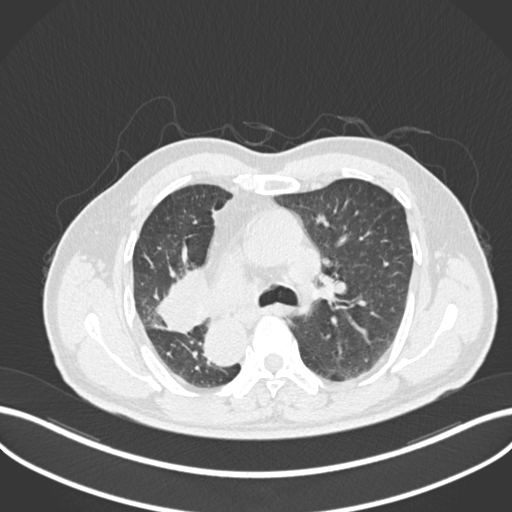
Chest CT, one axial slice; position 152 of 206 along the scan axis; 120 kVp; lung window (W 1500 / L -600 HU); 1 mm slice thickness; 512 × 512 image matrix. Patient: male, 67 years. From the clinical record (not read from this slice): clinical TNM (as recorded): T2a N0 M0.
Outlined on this slice (rectangle marked by the reading radiologist):
- lung tumour (recorded histology: squamous cell carcinoma): bounding box <155,262,211,336> (left, top, right, bottom; pixels)